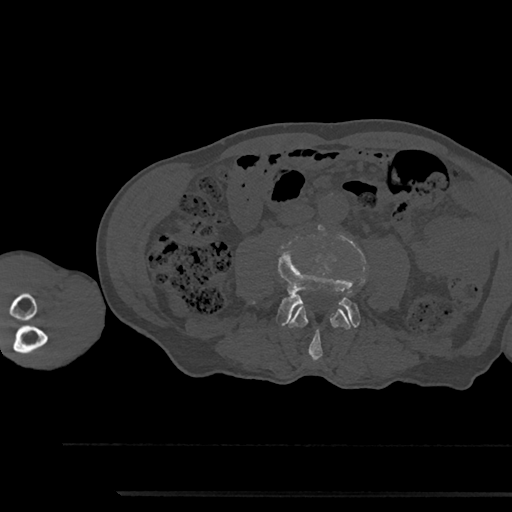
CT including the spine, one axial slice. Position 444 of 797 along the scan axis. Reconstruction kernel Br40s/3. 120 kVp. Bone window (W 1800 / L 400 HU). 0.5 mm slice thickness. 512 × 512 image matrix. Patient: male, 79 years. Case-level facts recorded for this patient, not image findings: primary cancer: prostate.
Annotated regions visible in this slice (semi-automatically segmented with operator editing):
- L3 vertebra: bounding box <288,304,351,360> (left, top, right, bottom; pixels)
- L4 vertebra: <277,248,359,327>